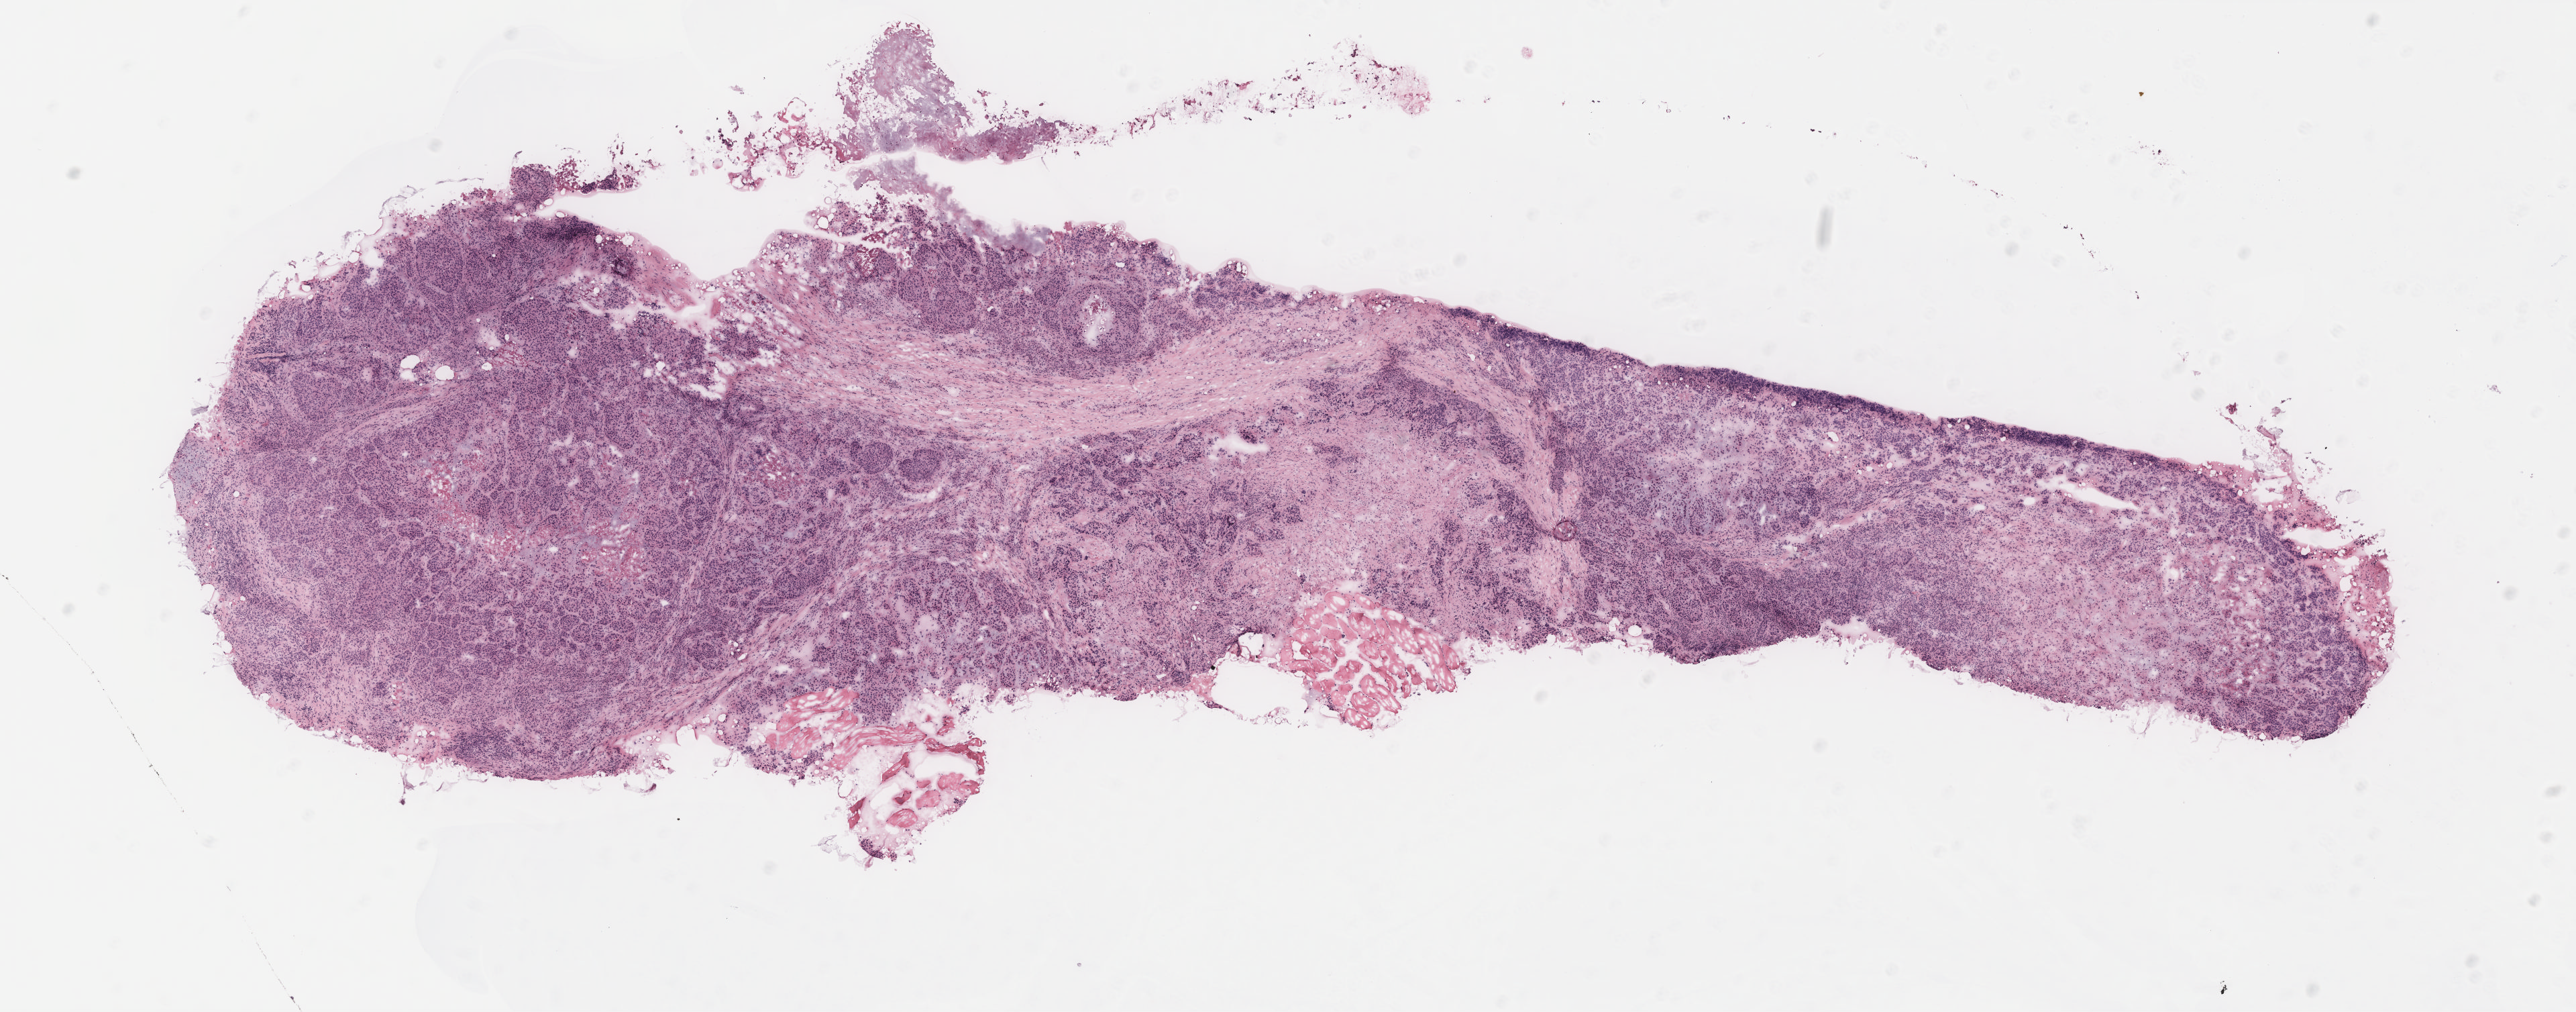
H&E-stained whole-slide image — whole scanned area (about 15.4 x 6.0 mm, acquisition: 40x scan) shown as a low-resolution overview. 64-year-old female patient.
* specimen: breast, tumour tissue